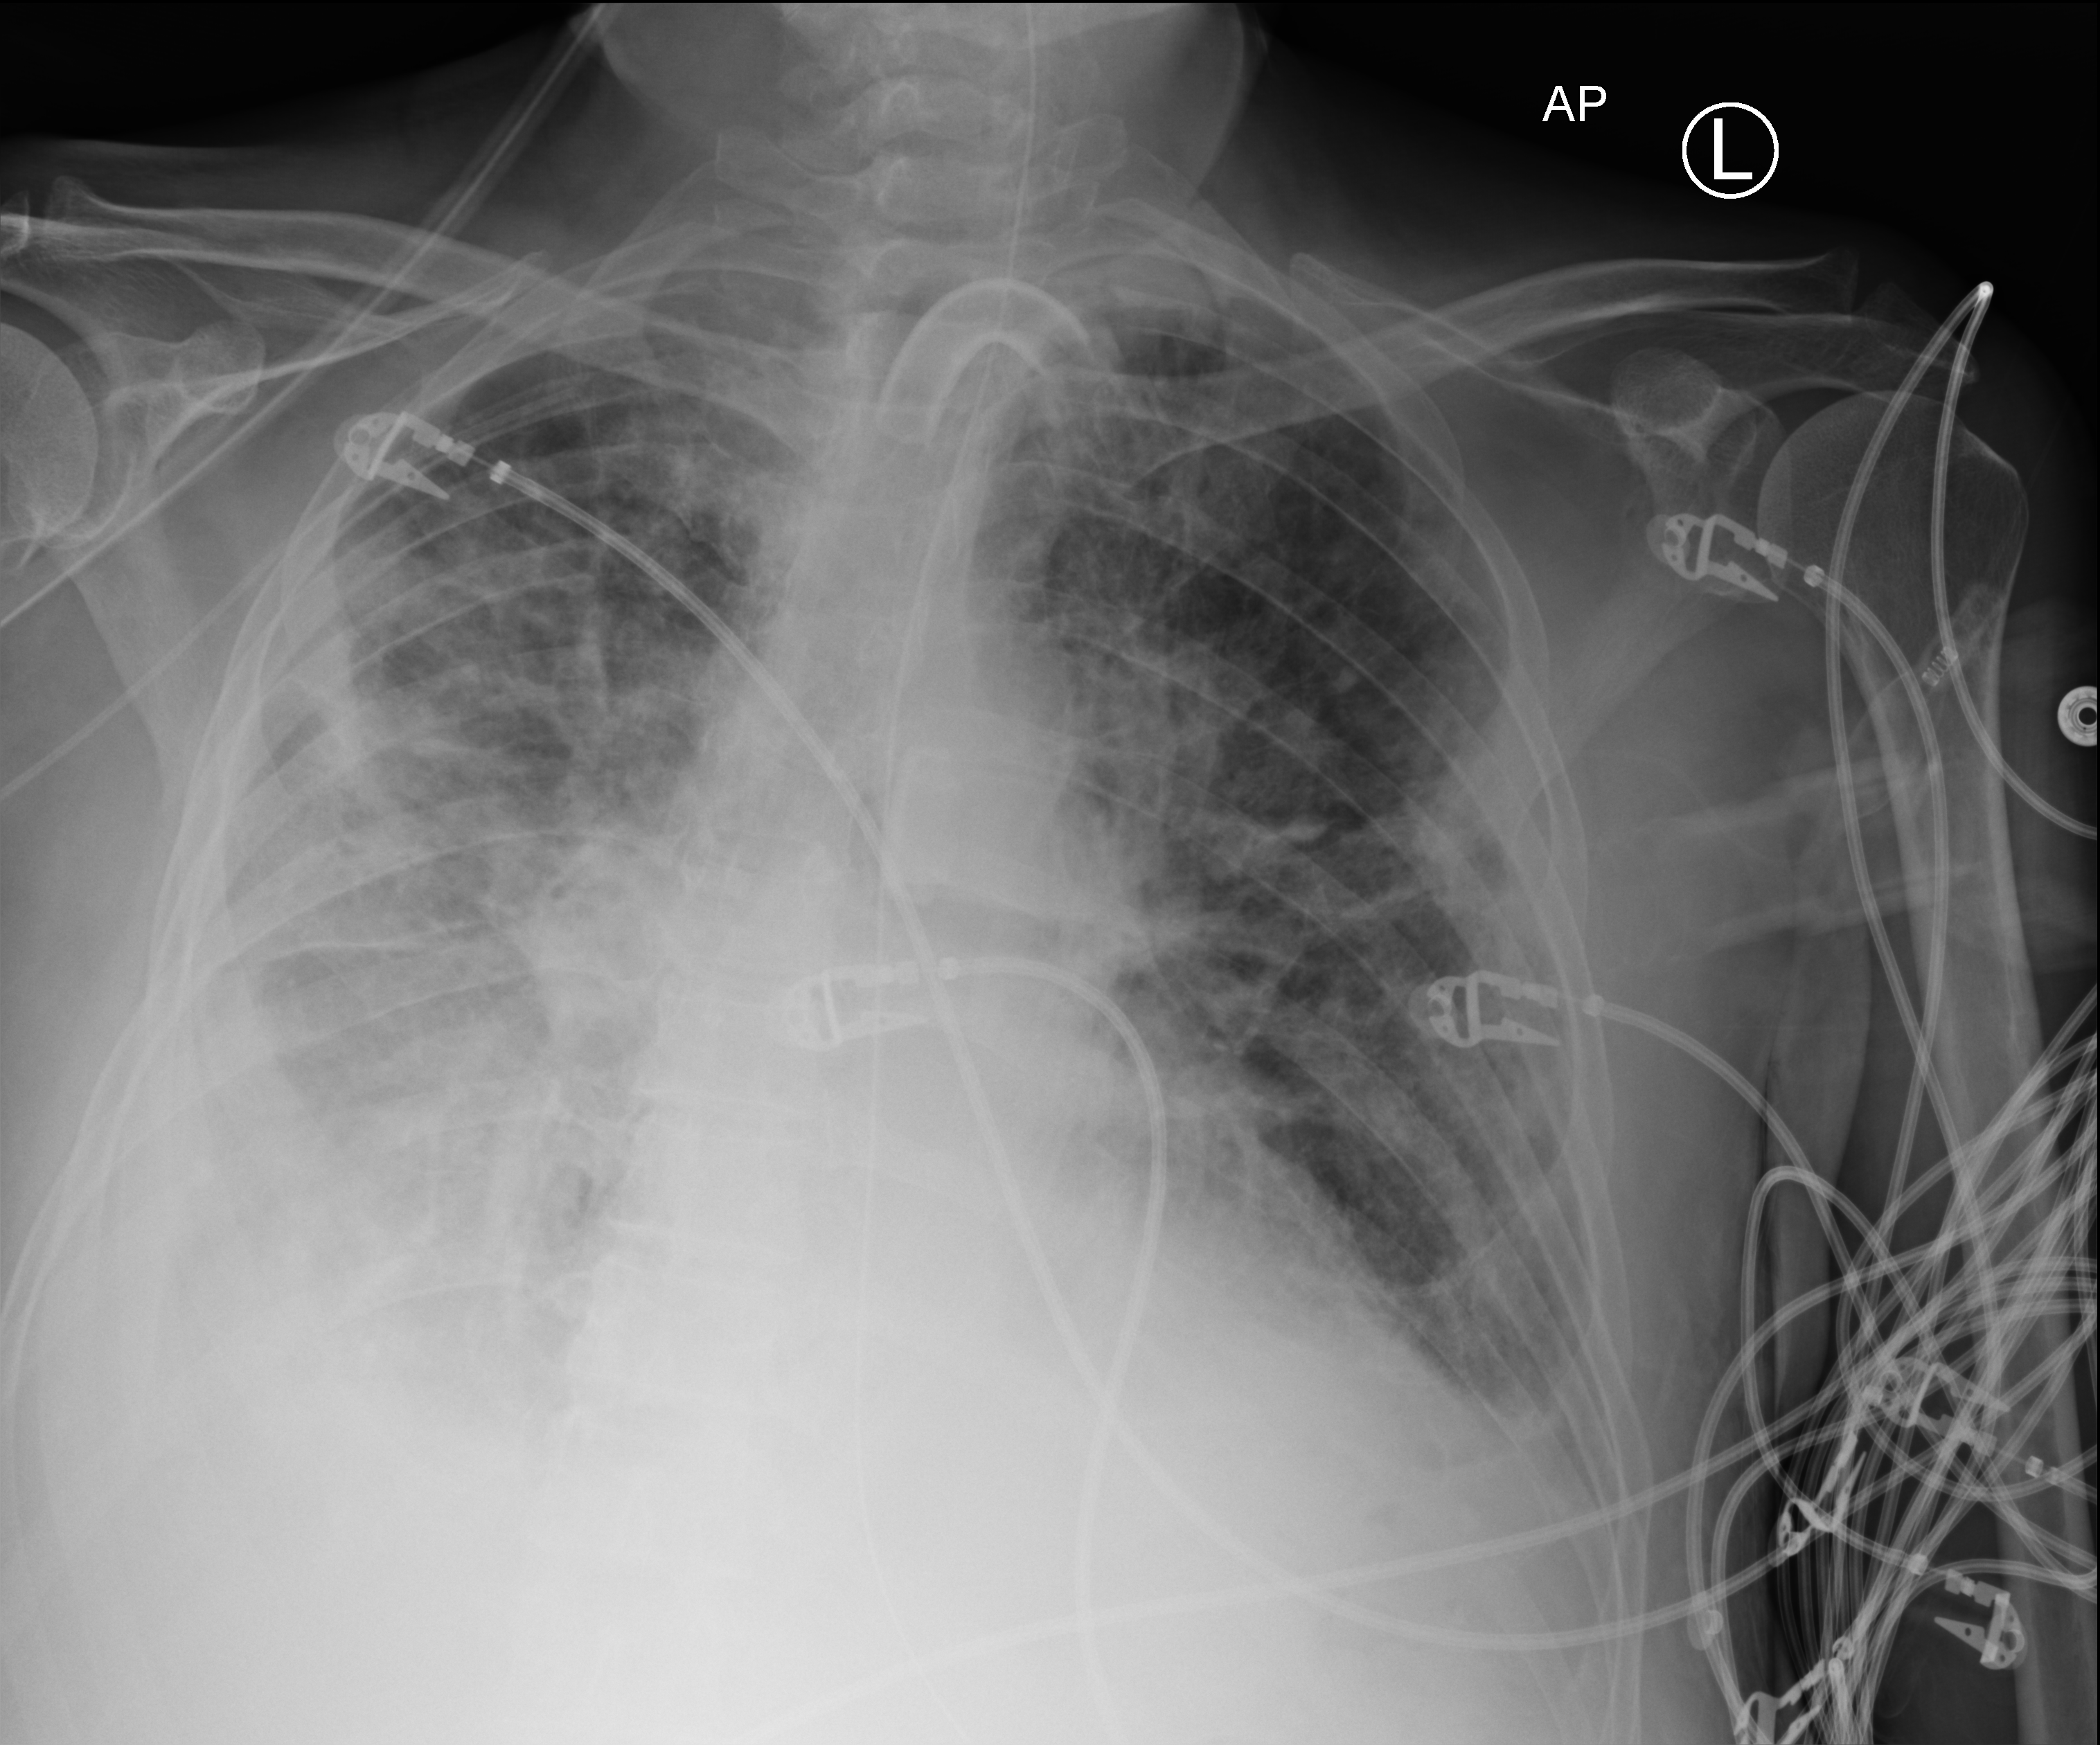
Portable chest radiograph; anteroposterior (AP) projection. Male patient hospitalised with COVID-19, age 75–90 years.
Admission-level facts for this patient (not findings on this image; timing relative to this image not recorded):
- chronic kidney disease (admission record): no
- other chronic lung disease (admission record): yes
- mechanically ventilated during this hospital stay: yes